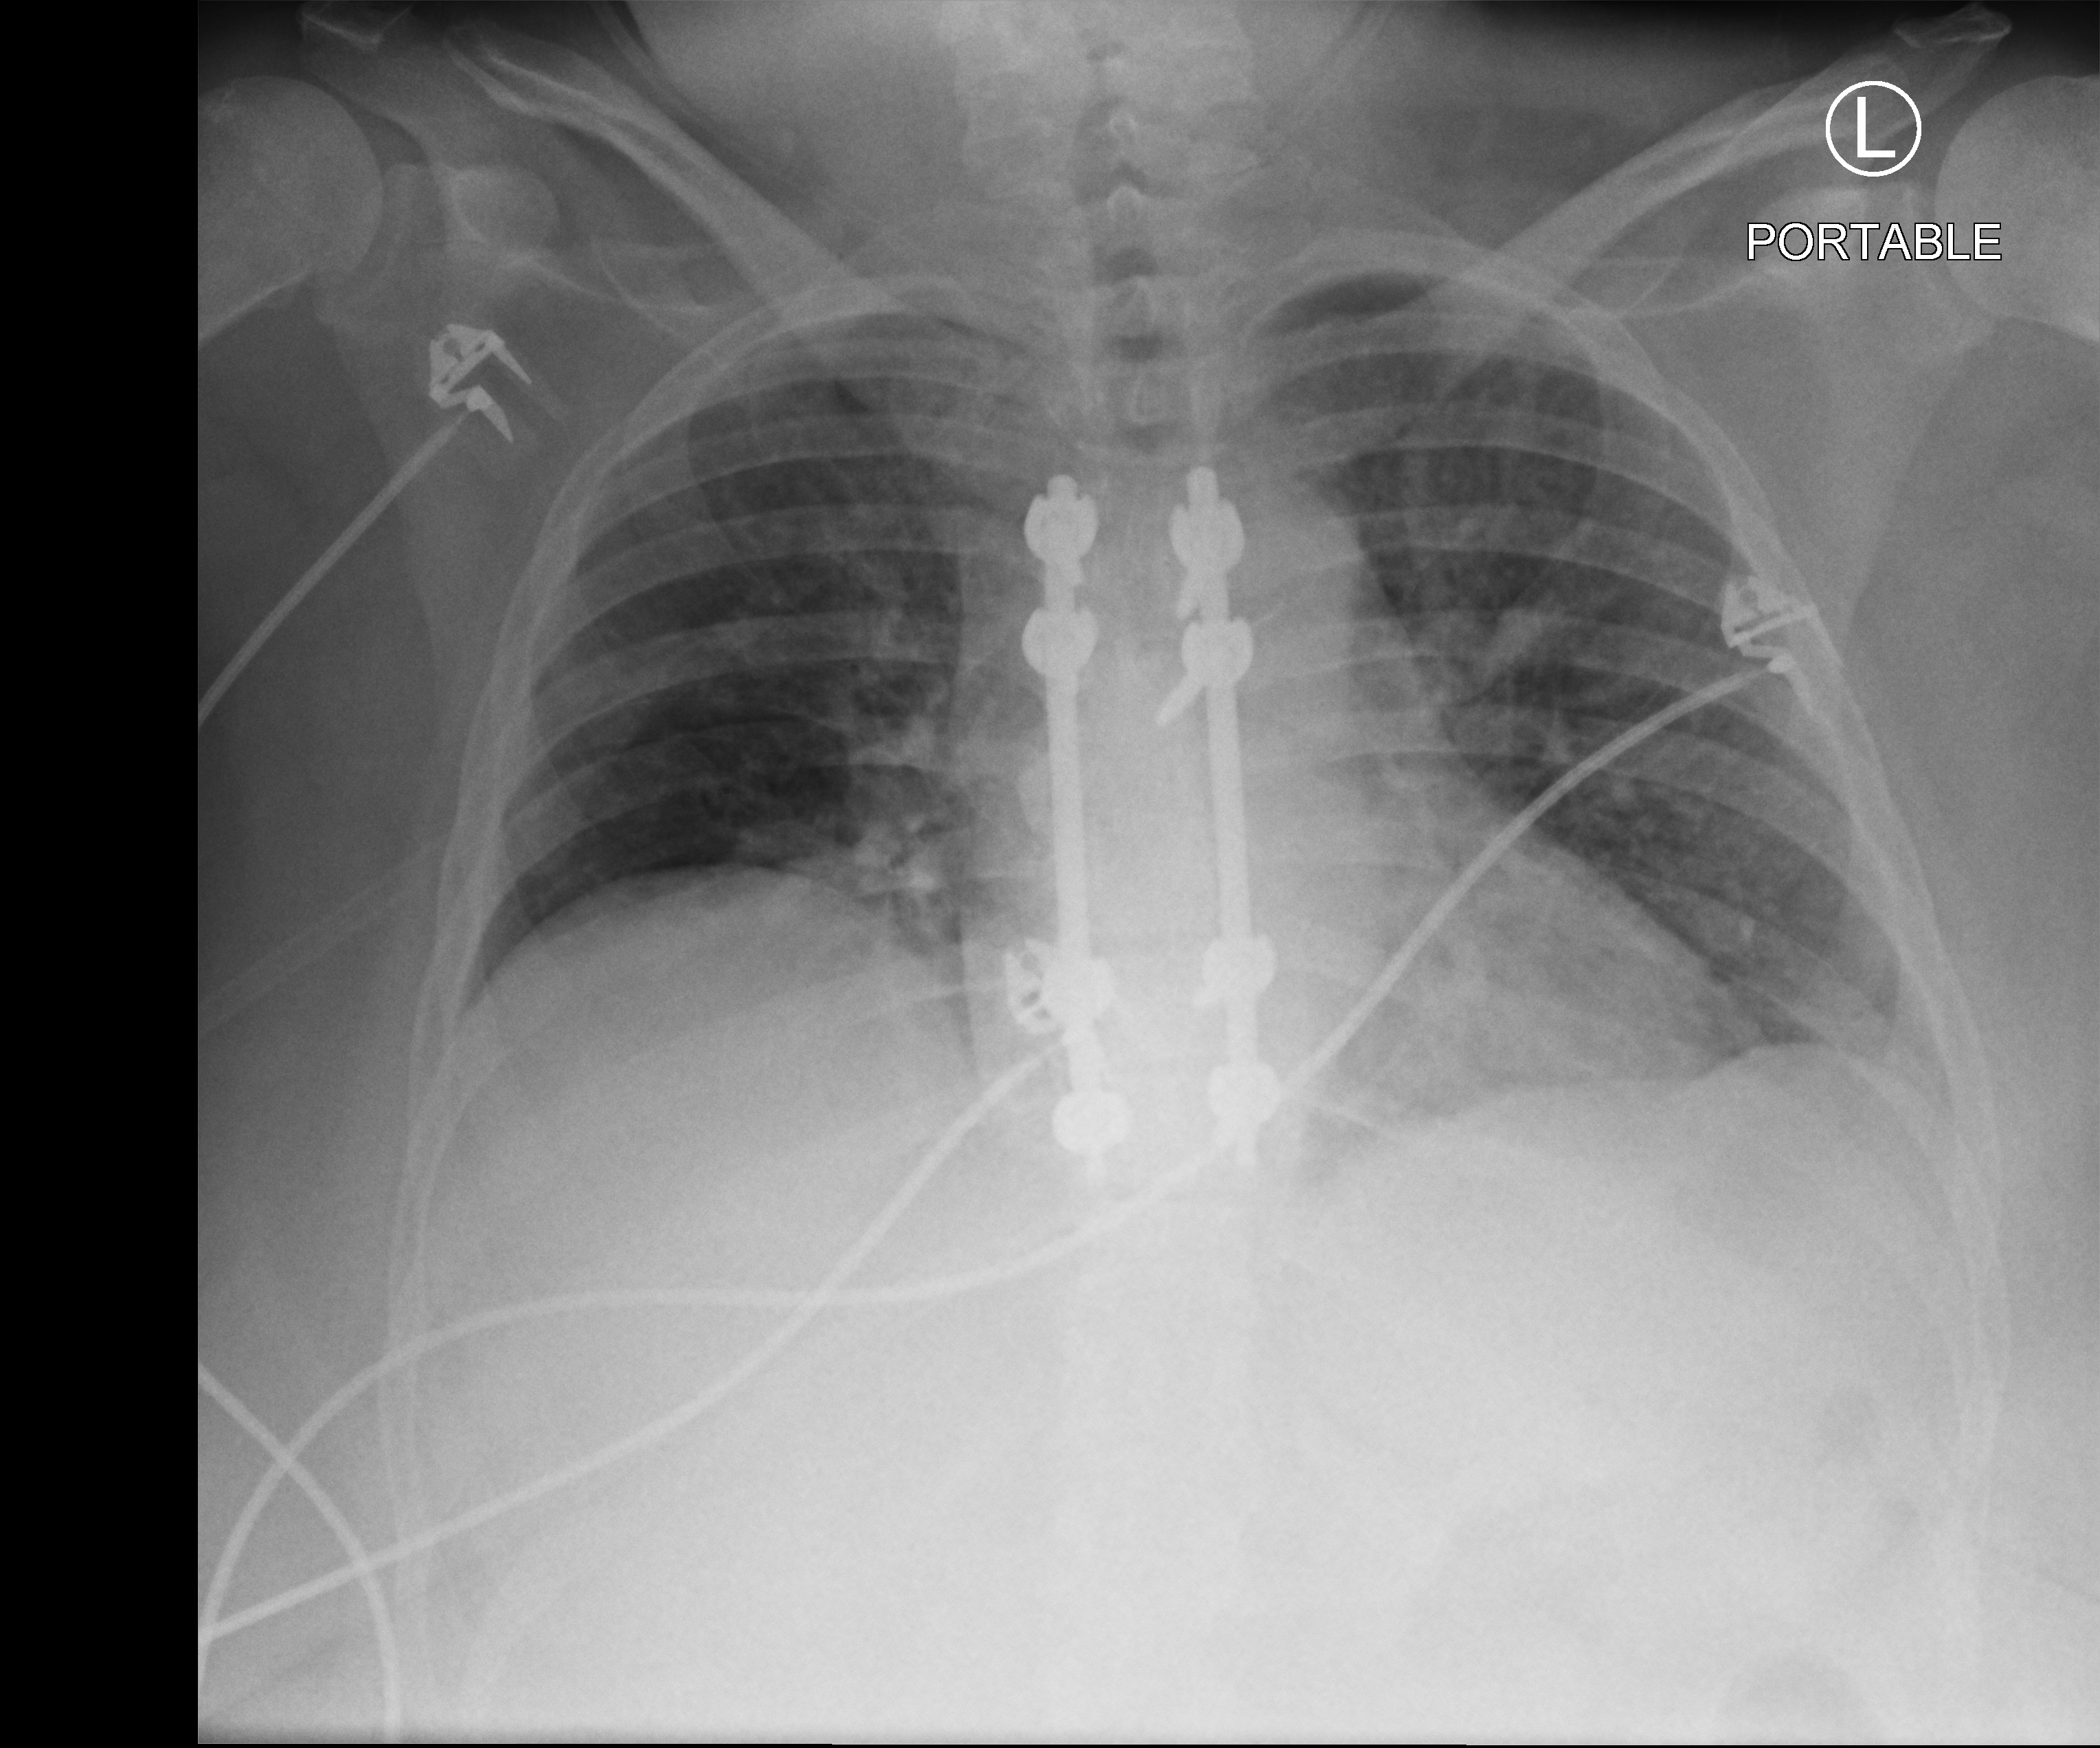
Bedside chest radiograph (computed radiography). Female patient hospitalised with COVID-19, age 18–59 years.
From the hospital-stay record, not from the radiograph (when in the stay this image was taken is not recorded):
- length of hospital stay: 19 days